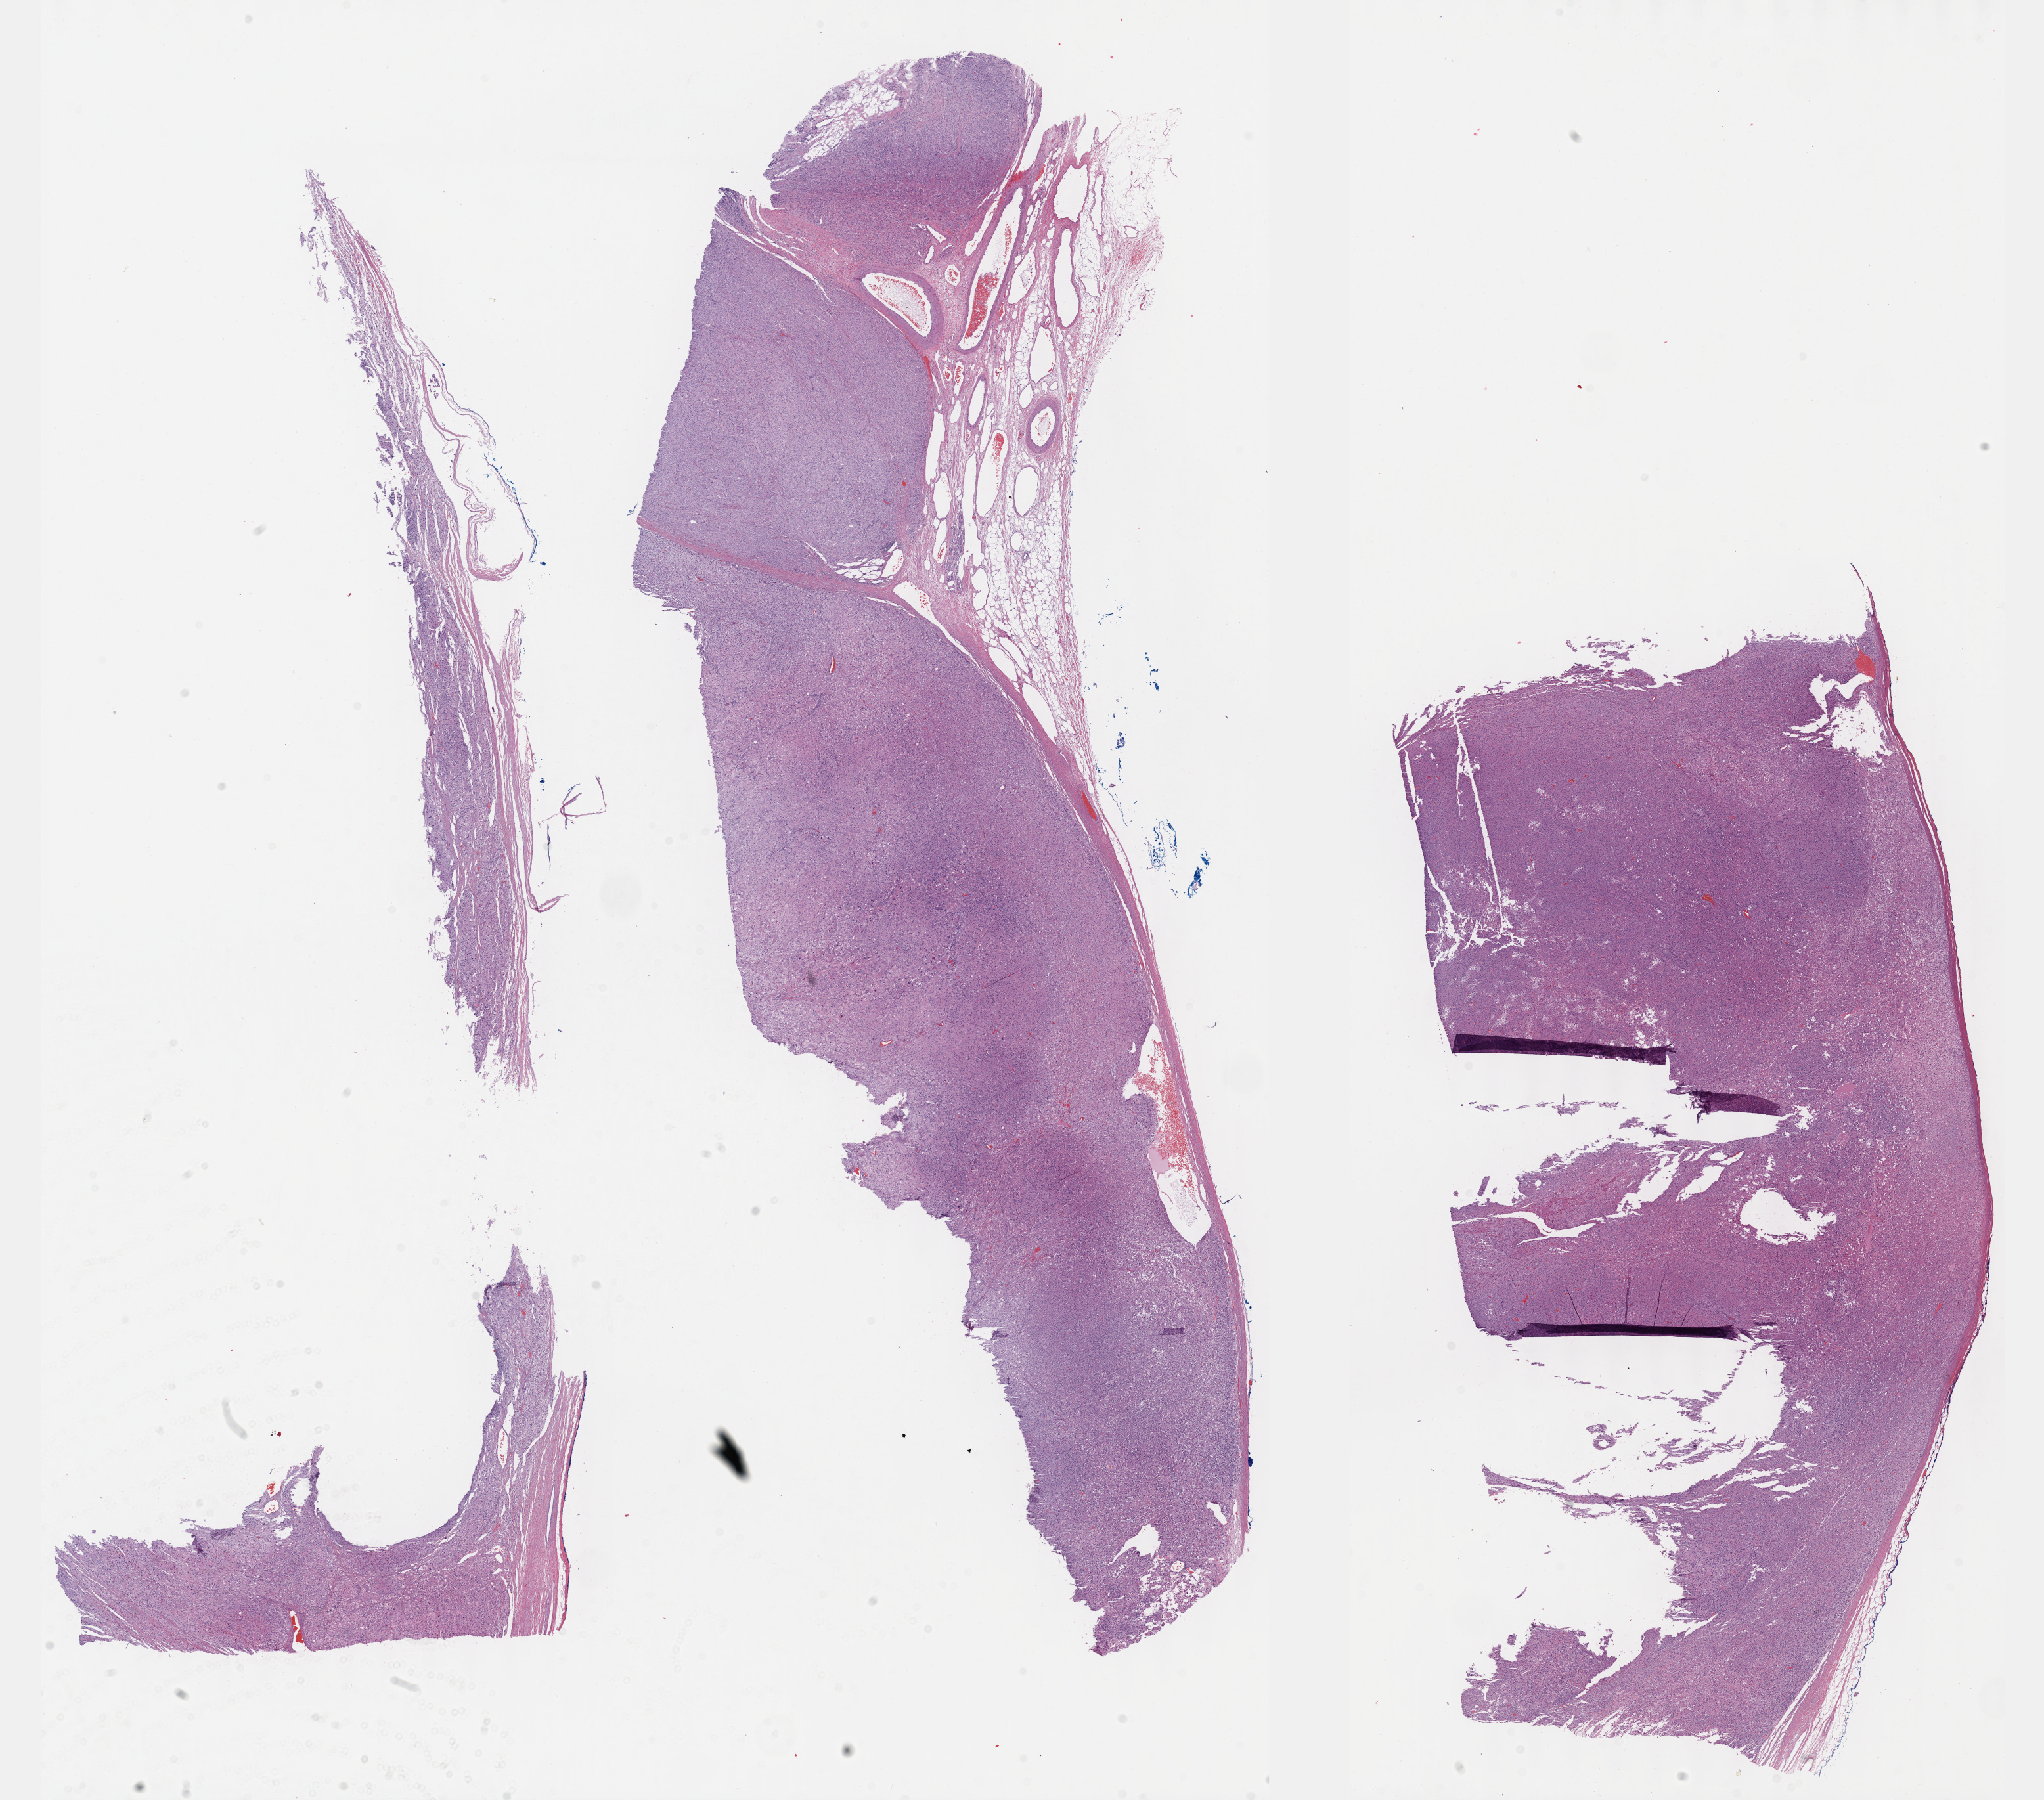
Whole-slide histology image, H&E — a low-resolution overview of the entire scanned area, about 25.1 x 22.2 mm (slide scanned at 40x), formalin-fixed paraffin-embedded (FFPE) diagnostic section, adrenal cortex, primary tumour sample. Female patient; age at initial diagnosis 53 years.
Lymph nodes positive (case pathology): 3 of 3 examined. Pathologic diagnosis: Adrenal cortical carcinoma (cortex of adrenal gland). Laterality: left.